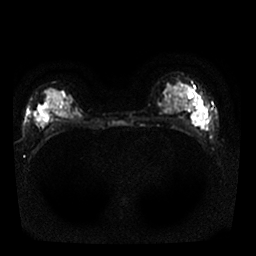
Breast MRI, one axial slice; slice 13 of 25 in the series (ordered by position); diffusion-weighted series; image 2 of 4 stored at this slice position (different b-values; order by instance number); 1.5 T; 4 mm slice thickness; 256 × 256 image matrix, field of view 320 × 320 mm. Female patient.
Outlined on this slice (outlined manually by an expert reader):
- tumour on diffusion-weighted imaging: box from (x=192, y=111) to (x=204, y=127) px